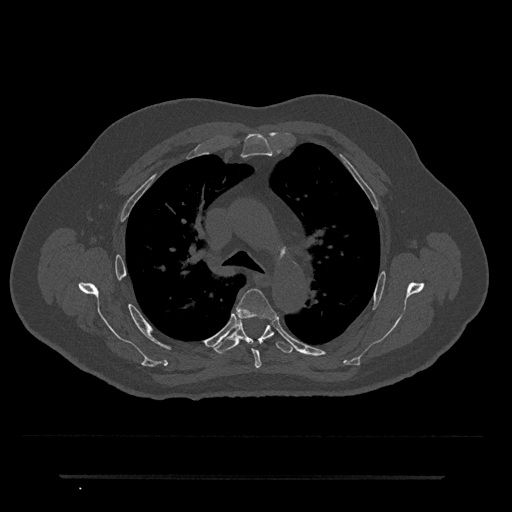
CT including the spine, one axial slice; position 505 of 797 along the scan axis; 120 kVp; bone window (W 1800 / L 400 HU); 0.5 mm slice thickness; 512 × 512 image matrix, field of view 437 × 437 mm. Male patient, age 69 years. From the clinical record (not read from this slice): primary cancer: prostate.
Annotated regions visible in this slice (semi-automatically segmented with operator editing):
- T4 vertebra: bounding box (x1, y1, x2, y2) in pixels: (236, 288, 277, 368)
- T5 vertebra: (212, 320, 293, 354)